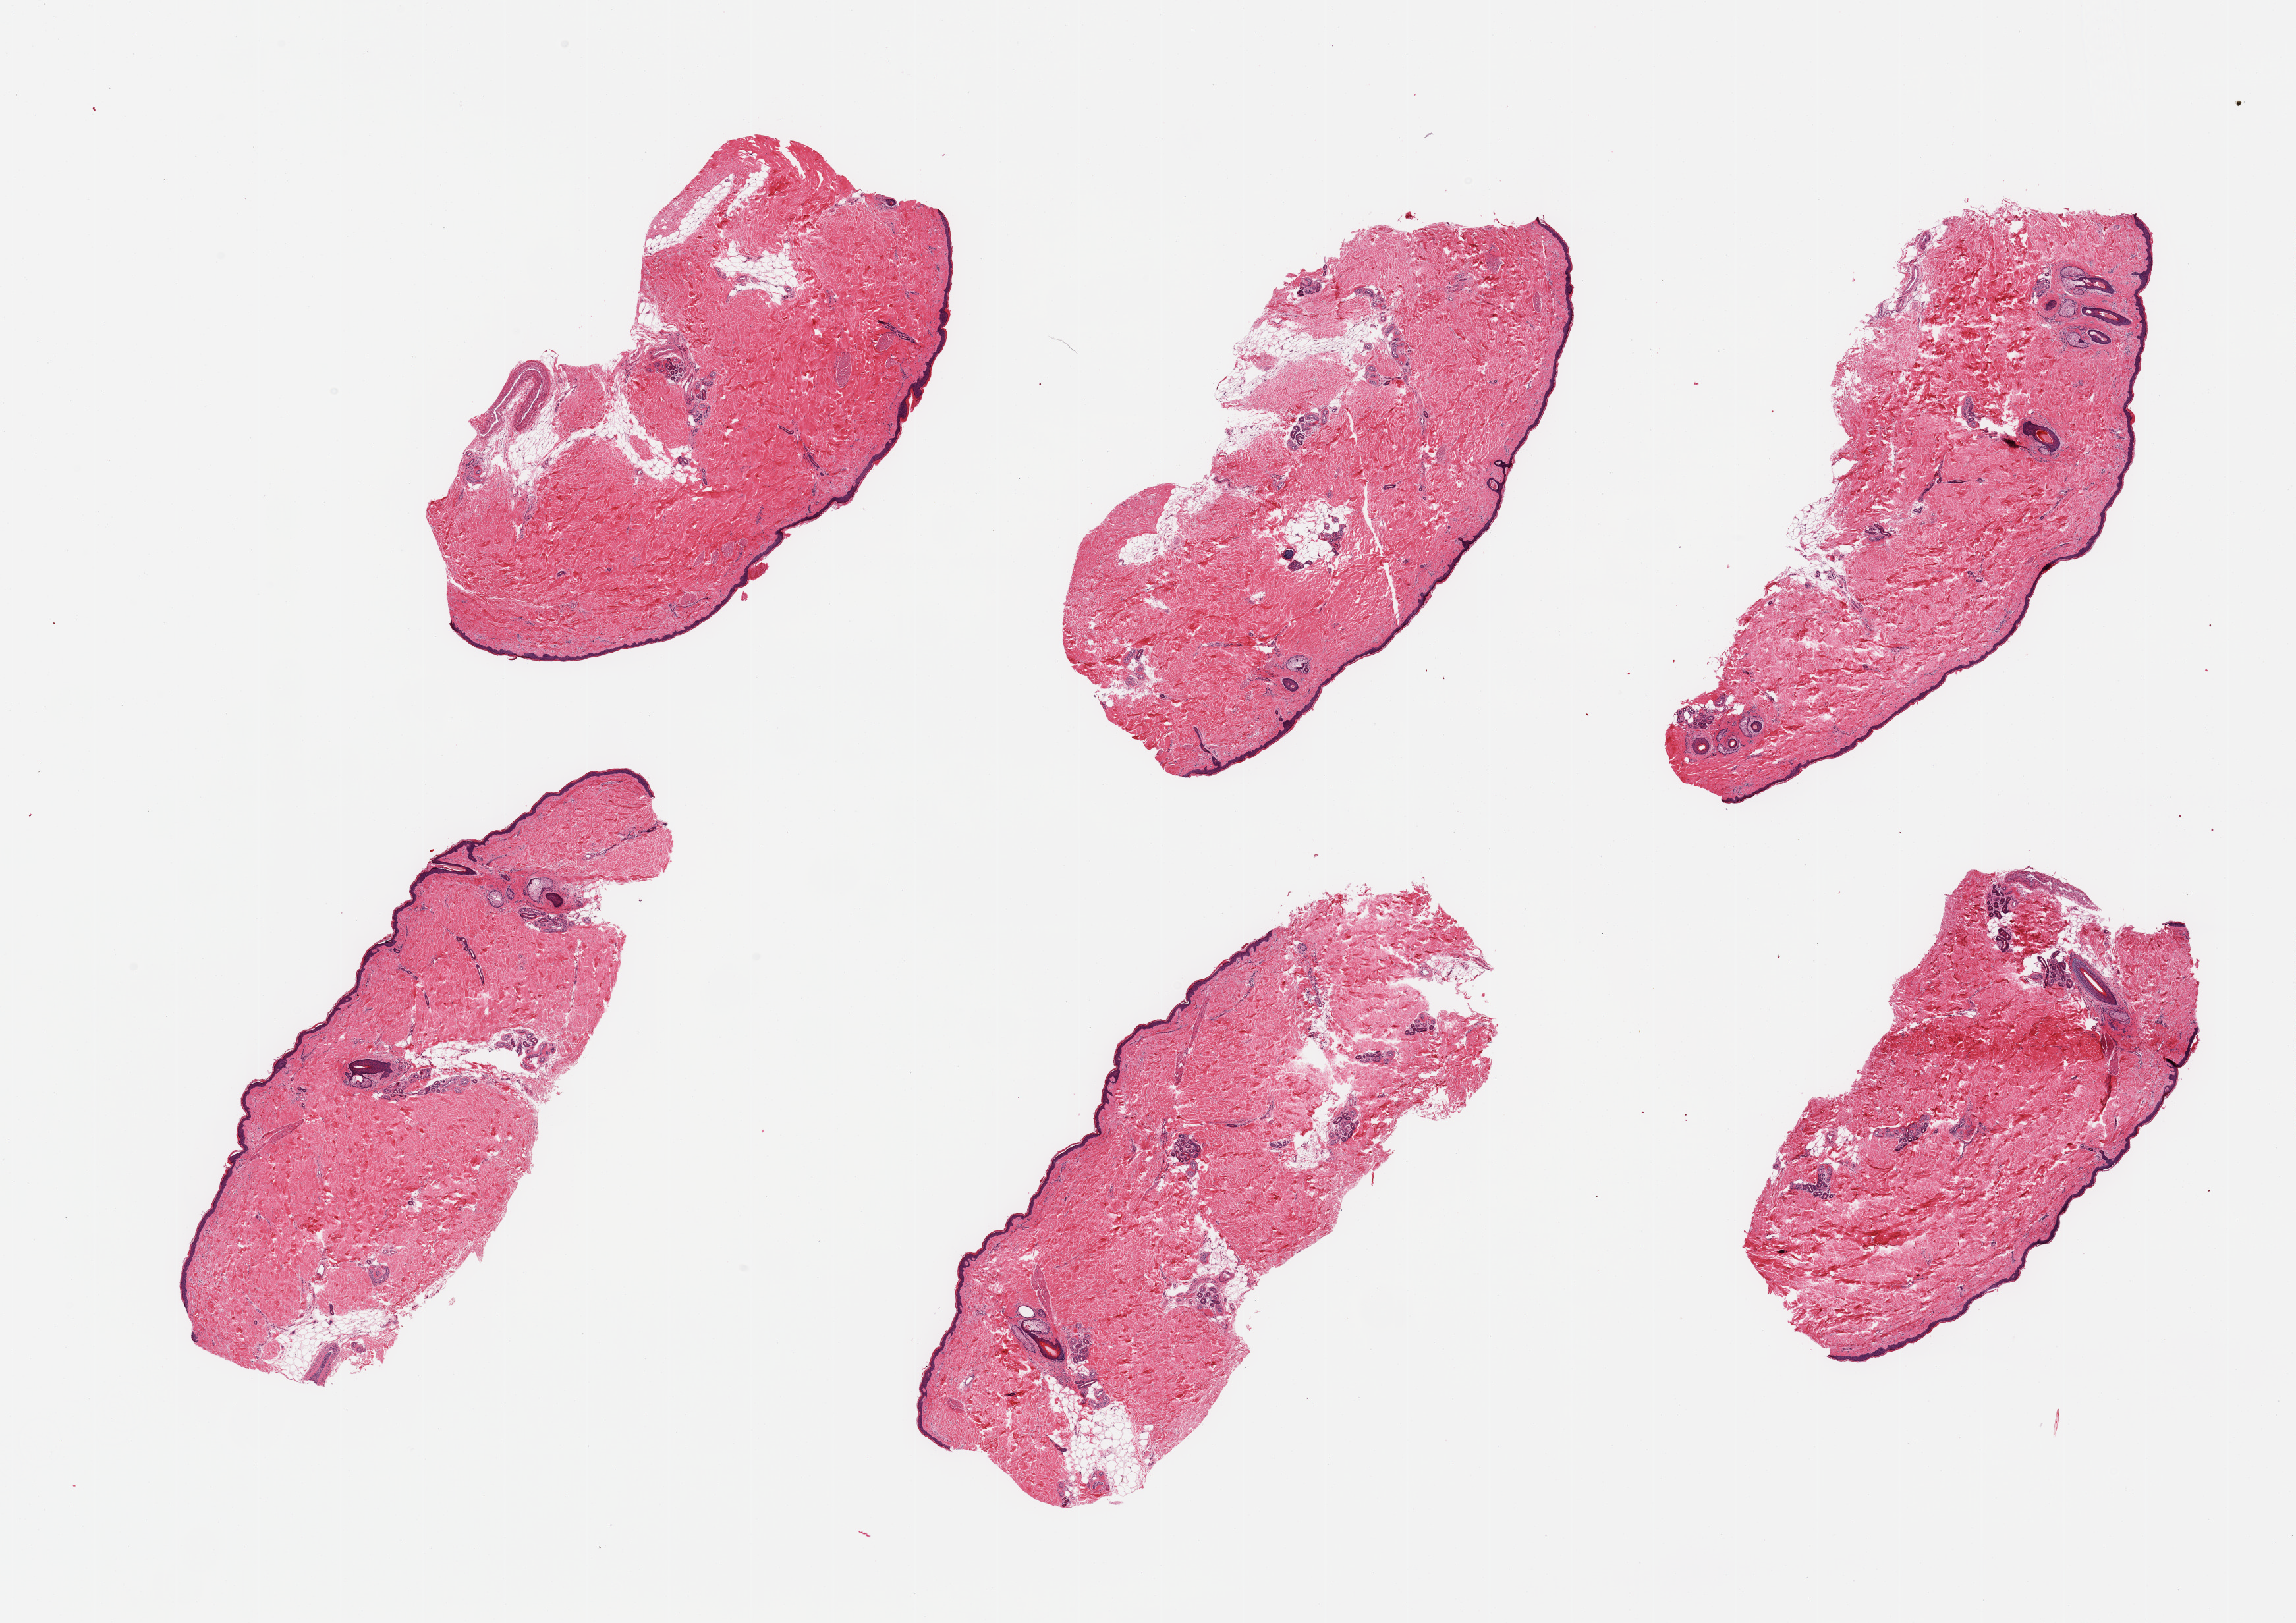
Whole-slide image, H&E stain, shown as a low-resolution overview of the whole scanned area (about 27.6 x 19.5 mm). PAXgene-fixed, paraffin-embedded tissue. Target tissue: skin of lower leg. Tissue donor sample. Donor sex: male.
Pathologist's review note for this sample: 6 pieces, trace dermal fat; squamous epithelium is ~40-50 microns.